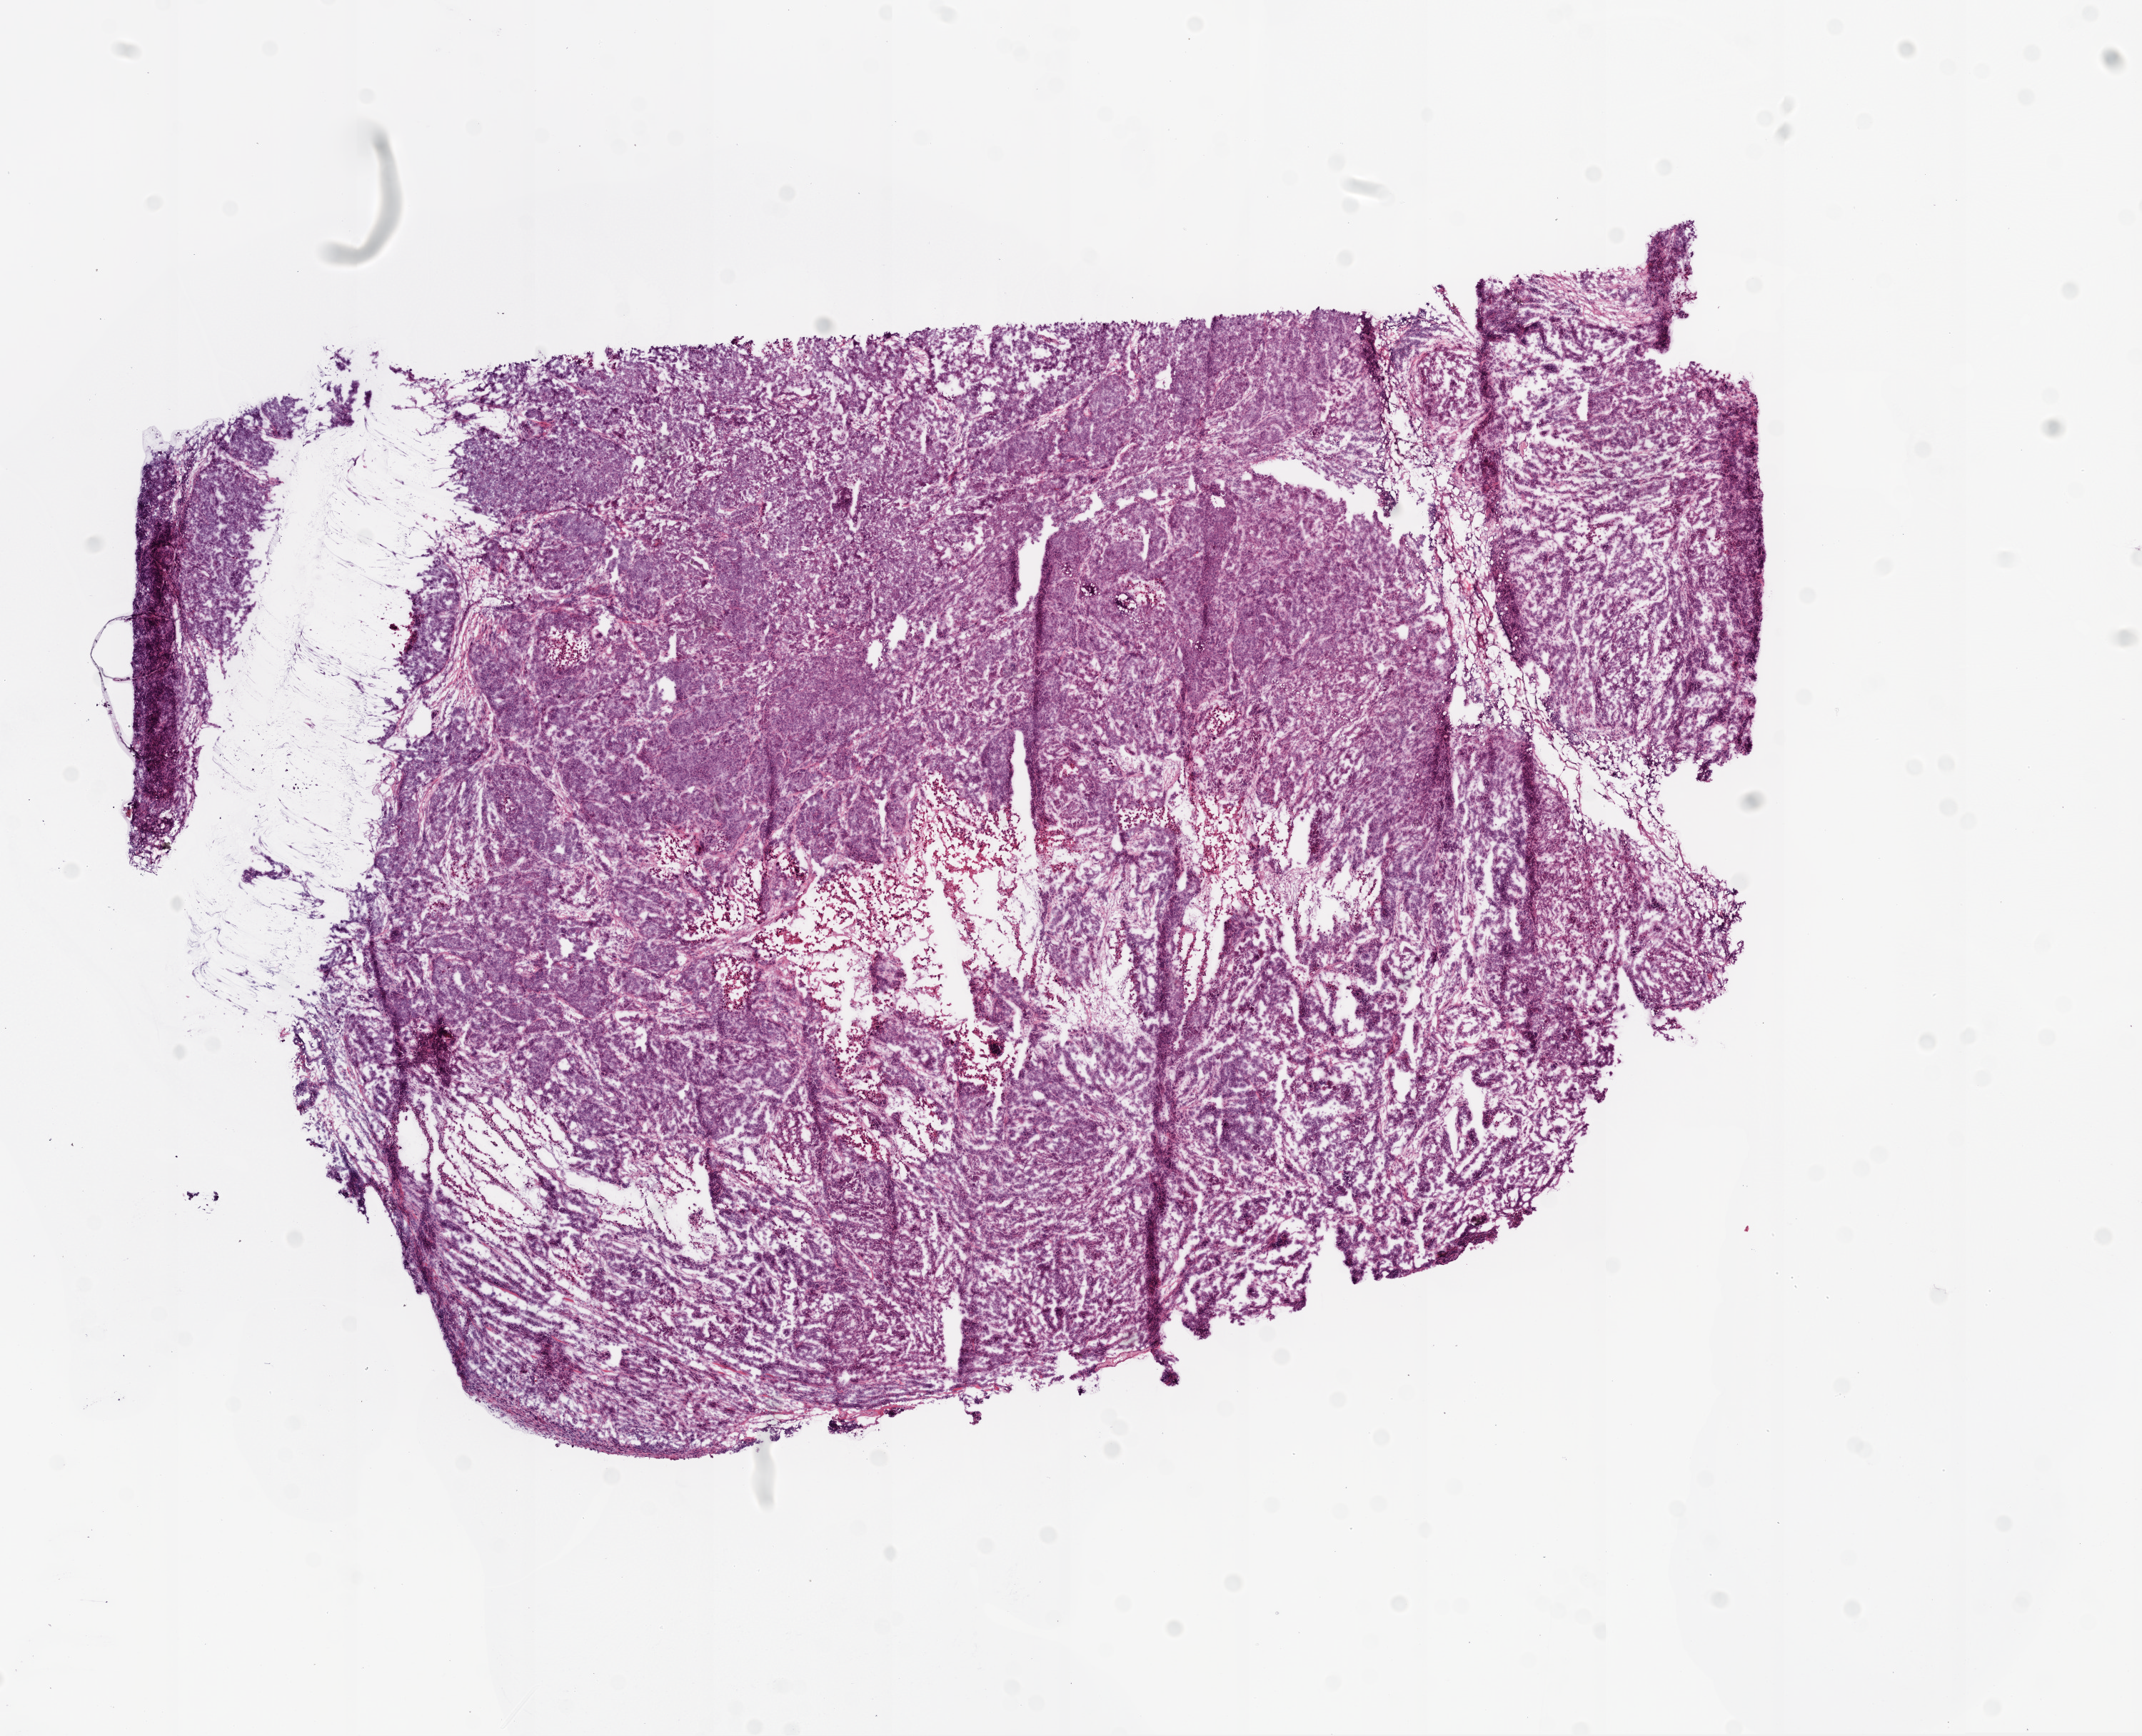
Digitized H&E-stained tissue section (whole slide) — whole scanned area (about 12.0 x 9.8 mm, acquisition: 20x scan) shown as a low-resolution overview. Frozen section. Ovary, primary tumour sample. Patient: female, age at initial diagnosis 70 years. Histologic grade: G3 (poorly differentiated). Pathologist review of this section (percent, as recorded): tumour cells 85%, tumour nuclei 90%, normal cells 0%, stromal cells 10%, necrosis 5%.
• FIGO stage: IIIC
• histologic diagnosis: Serous cystadenocarcinoma, NOS